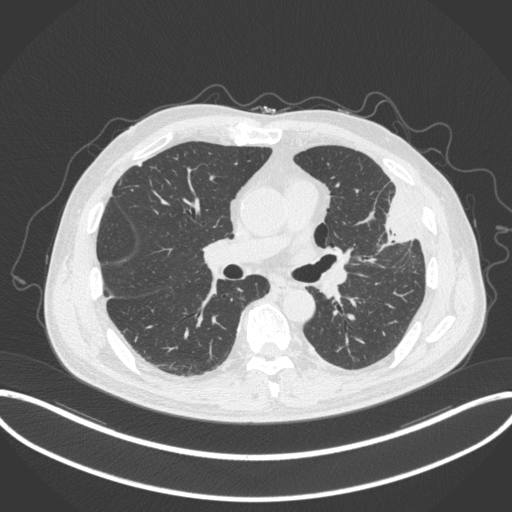
Chest CT, one axial slice. Position 184 of 382 along the scan axis. Reconstruction kernel B31f. Lung window (W 1500 / L -600 HU). 1 mm slice thickness. 512 × 512 image matrix. Patient: male, 64 years. From the clinical record (not read from this slice): clinical TNM (as recorded): T4 N1 M0; histopathological grade: G3.
Structures marked on this image (rectangle marked by the reading radiologist):
- lung tumour (recorded histology: adenocarcinoma): bounding box (x1, y1, x2, y2) in pixels: (370, 189, 418, 246)